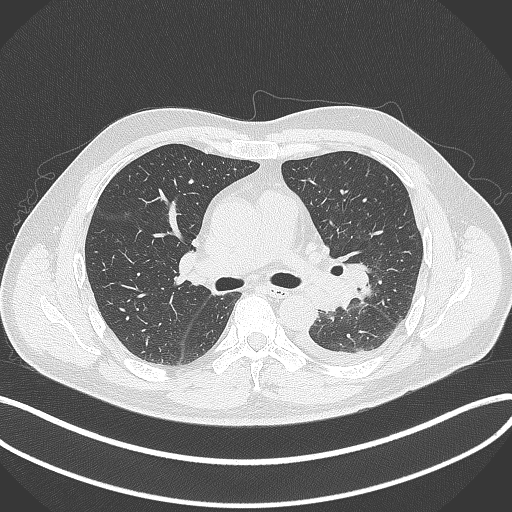
Chest CT, one axial slice; position 216 of 342 along the scan axis; 120 kVp; lung window (W 1500 / L -600 HU); 1 mm slice thickness; 512 × 512 image matrix, field of view 400 × 400 mm. Male patient, age 58 years. From the clinical record (not read from this slice): clinical TNM (as recorded): T3 N1 M1b.
Annotated regions visible in this slice (rectangle marked by the reading radiologist):
- lung tumour (recorded histology: small cell carcinoma): box from (x=341, y=260) to (x=371, y=293) px